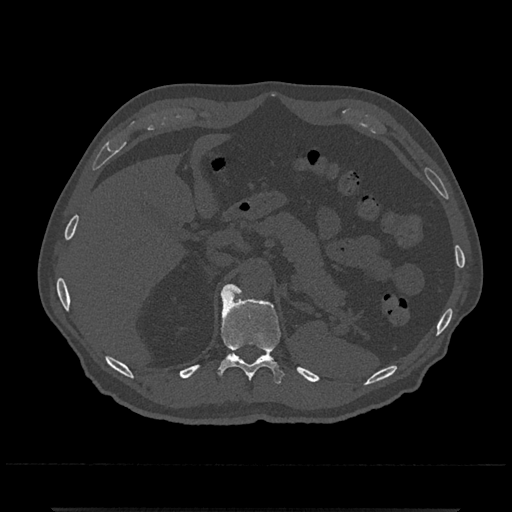
CT including the spine, one axial slice; position 486 of 797 along the scan axis; reconstruction kernel Br40s/3; 120 kVp; bone window (W 1800 / L 400 HU); 512 × 512 image matrix, field of view 393 × 393 mm. Male patient, age 67 years. Case-level facts recorded for this patient, not image findings: primary cancer: prostate.
Outlined on this slice (semi-automatically segmented with operator editing):
- T11 vertebra: bounding box <220,290,284,384> (left, top, right, bottom; pixels)
- T12 vertebra: <222,284,242,296>